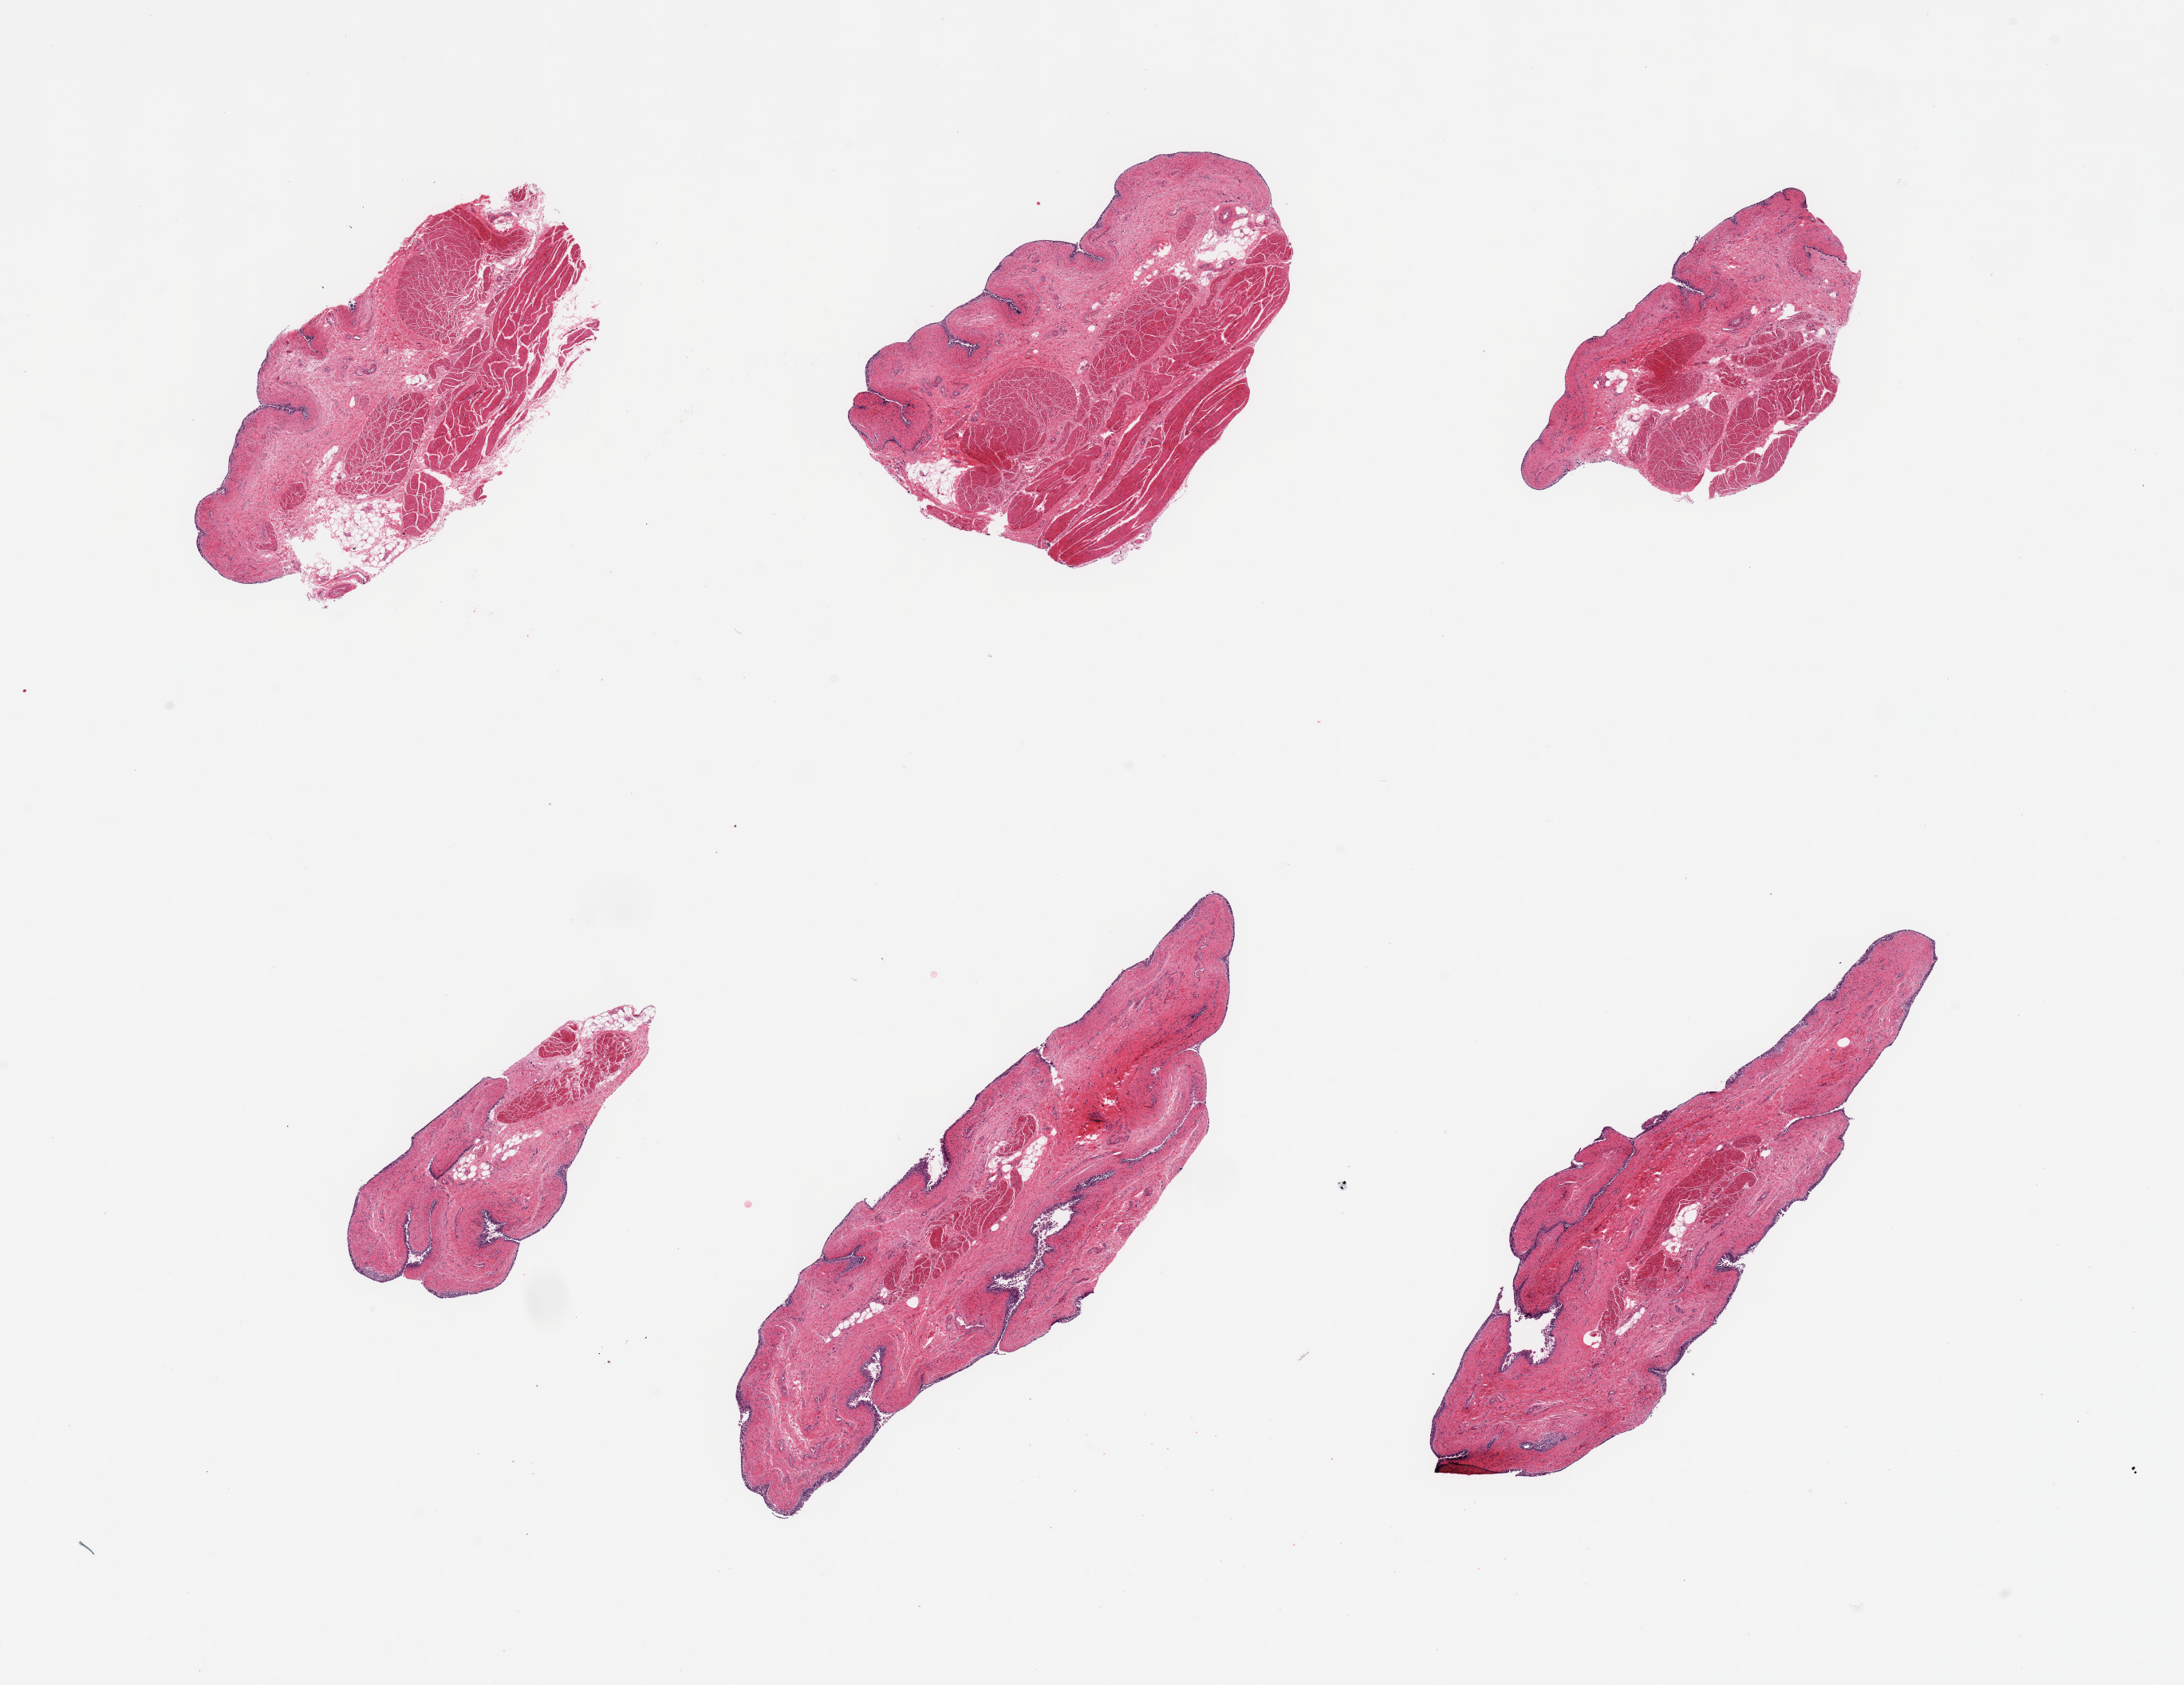
Digitized haematoxylin and eosin-stained section, brightfield — shown as a low-resolution overview of the whole scanned area (about 21.7 x 16.7 mm); PAXgene-fixed, paraffin-embedded tissue; section of vagina (target tissue); tissue donor sample. Donor: female.
Reviewer comment on this tissue sample: 6 pieces, target mucosa moderately autolyzed, sloughing, up to ~25 microns residual.